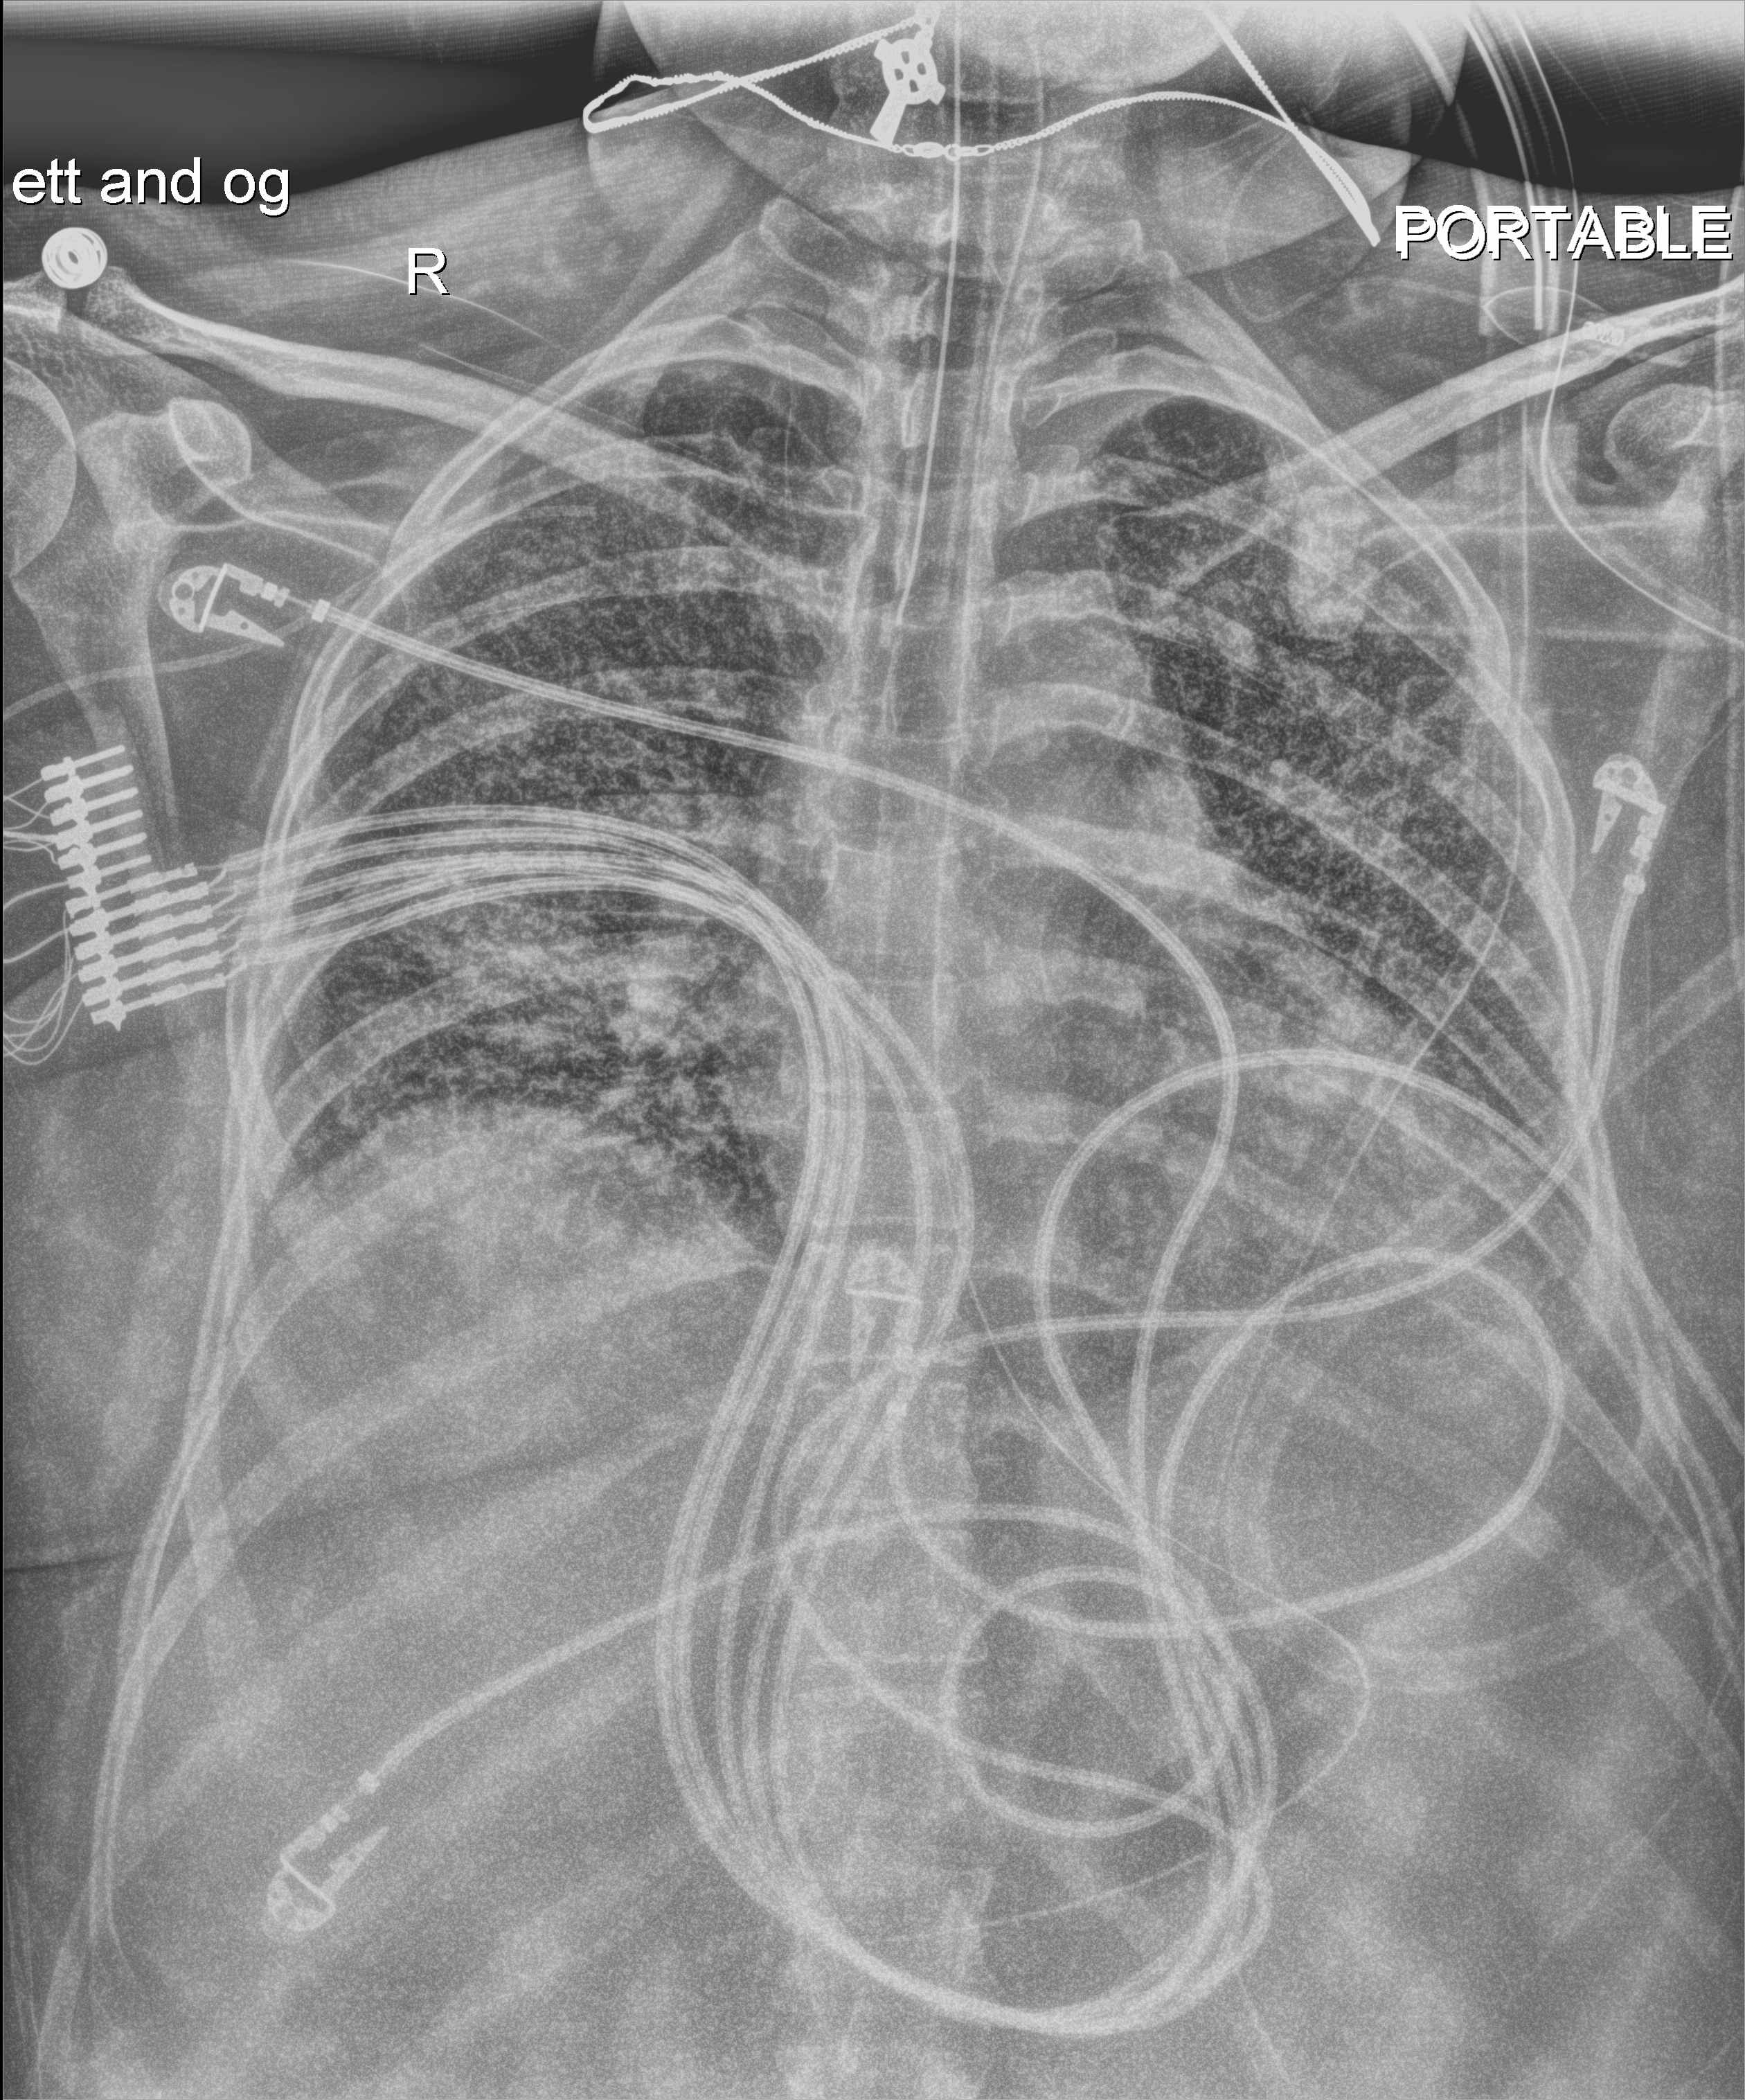
Chest X-ray (portable); anteroposterior (AP) projection. Patient hospitalised with COVID-19; female, aged 18–59 years.
From the hospital-stay record, not from the radiograph (when in the stay this image was taken is not recorded):
- mechanically ventilated during this hospital stay: yes
- other chronic lung disease (admission record): yes